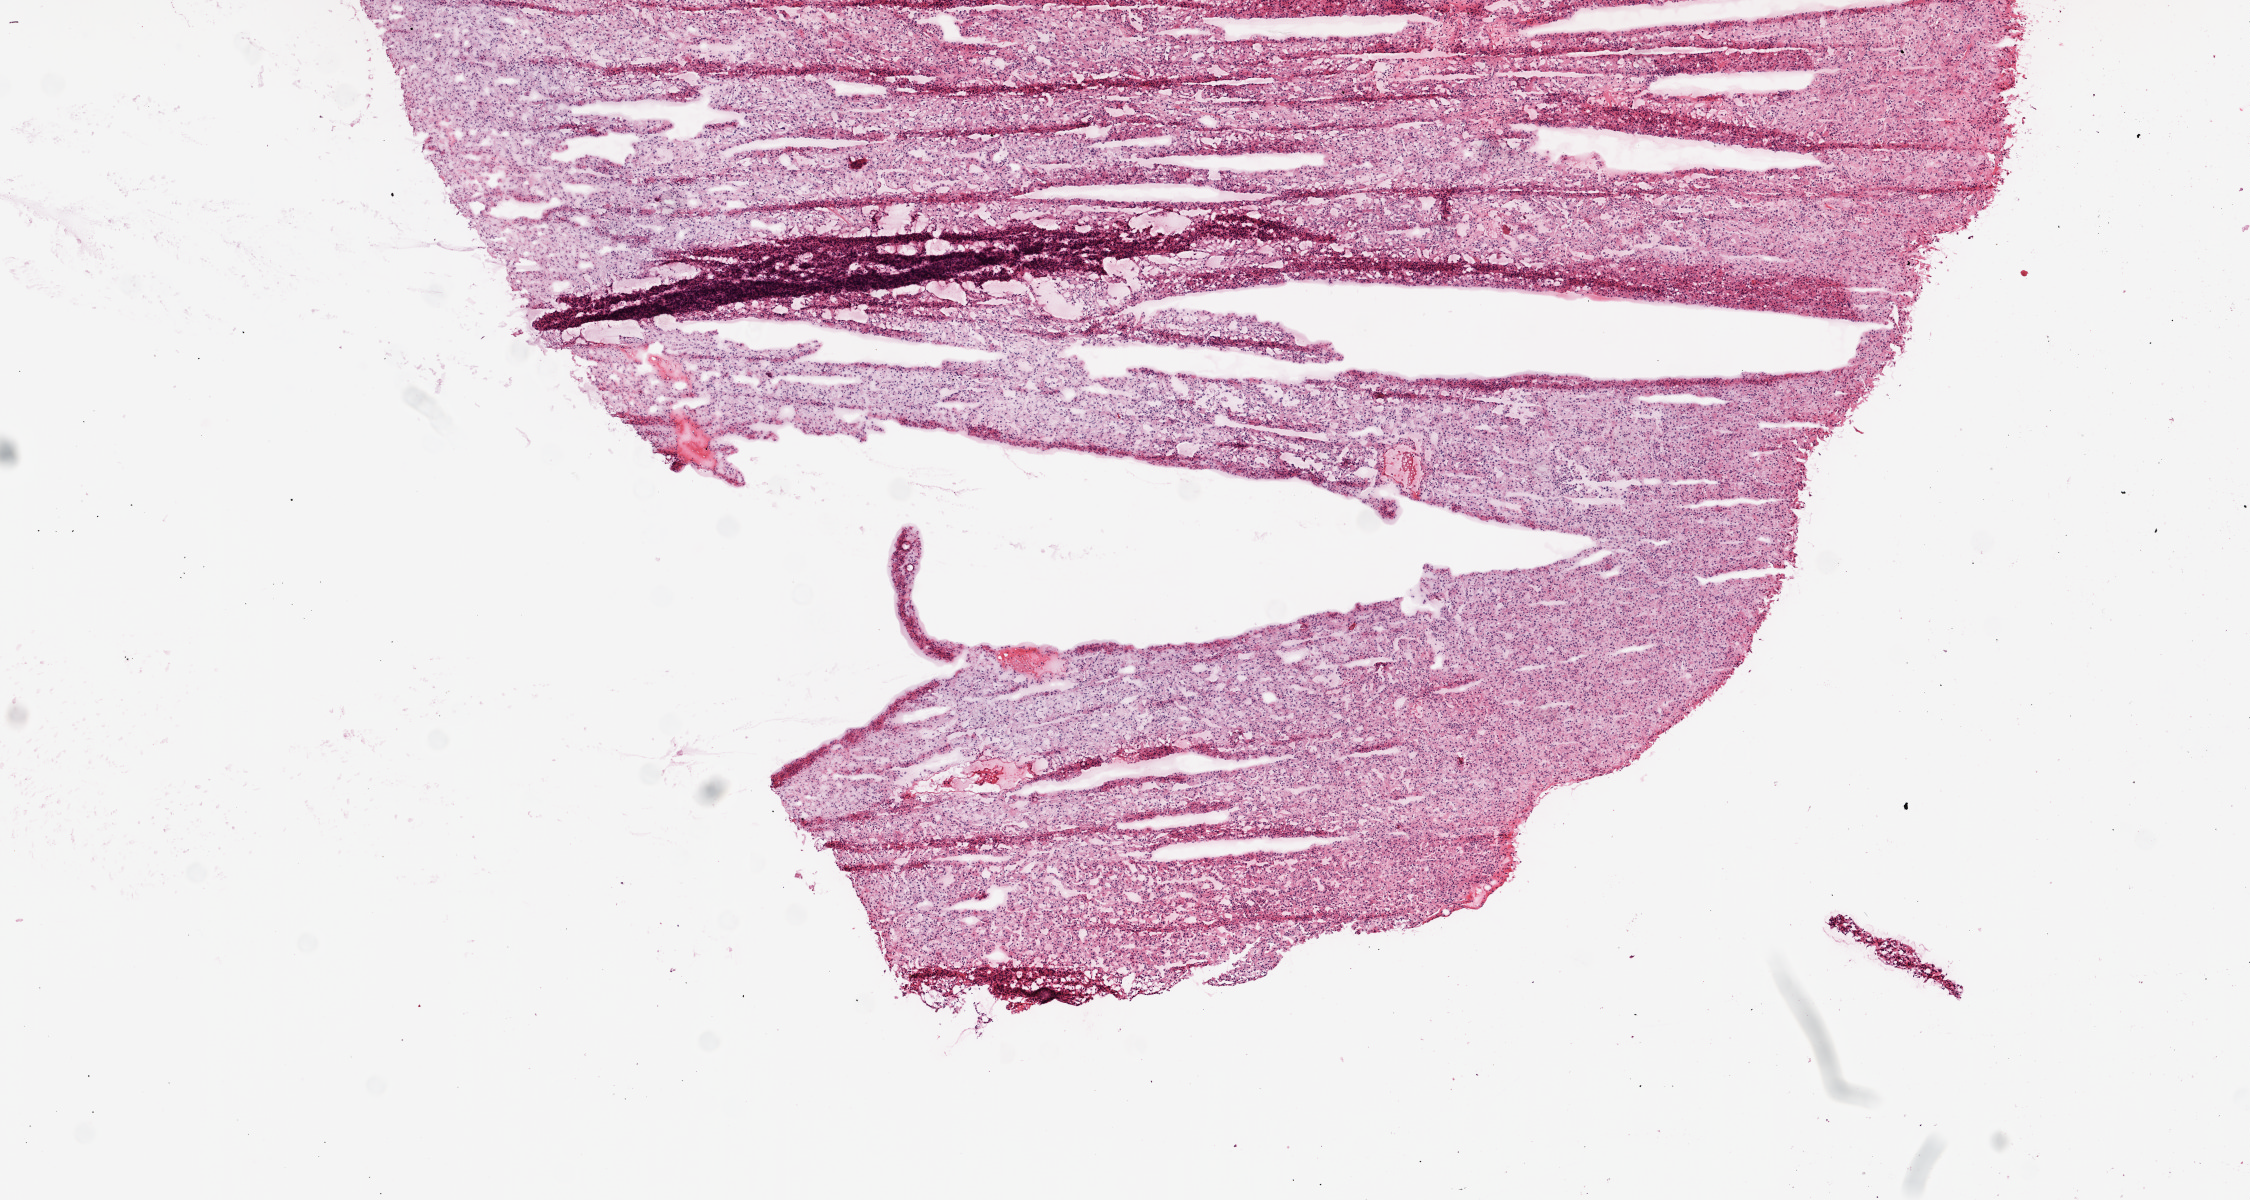
Hematoxylin and eosin (H&E) stained whole-slide image — whole scanned area (about 9.0 x 4.8 mm) shown as a low-resolution overview, frozen section from the top of the tissue portion, primary tumour sample from the kidney. Patient: male, age at initial diagnosis 60 years. Histologic grade: G3 (poorly differentiated). Pathologist review of this section (percent, as recorded): tumour cells 95%, tumour nuclei 90%, normal cells 0%, stromal cells 5%, necrosis 0%.
Histologic diagnosis: Clear cell adenocarcinoma, NOS. AJCC pathologic stage: IV. Laterality: left.